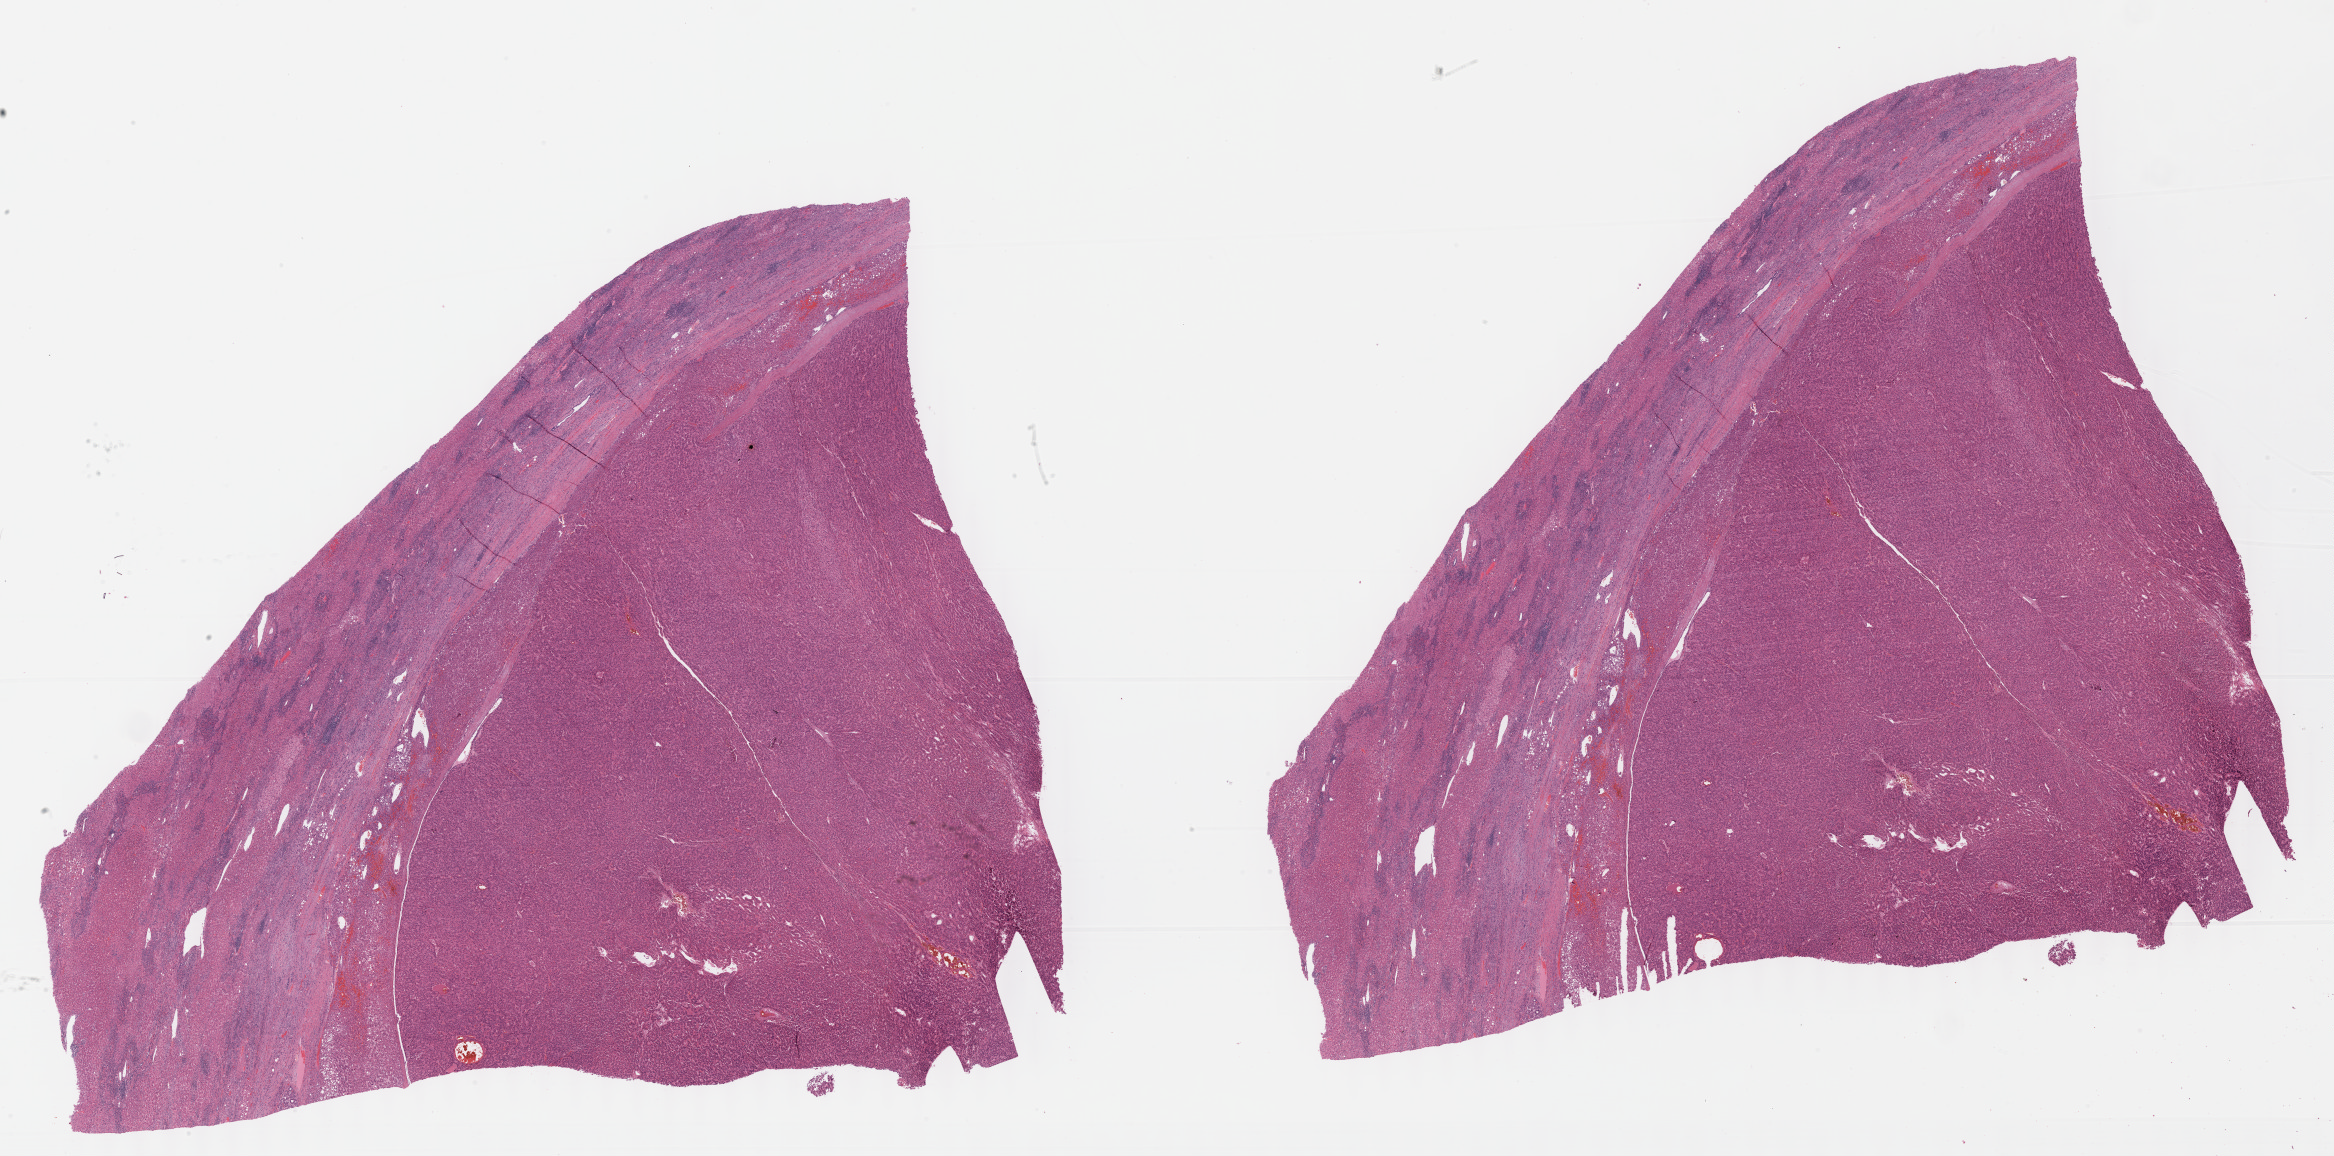
Whole-slide histology image, H&E, a low-resolution overview of the entire scanned area, about 37.7 x 18.7 mm (slide scanned at 40x). FFPE section. Sample: primary tumour, liver. Patient: female, age at initial diagnosis 83 years. Histologic grade: G1 (well differentiated).
TNM: T1 N0 M0. AJCC pathologic stage: I (7th edition). Histologic diagnosis: Hepatocellular carcinoma, NOS.